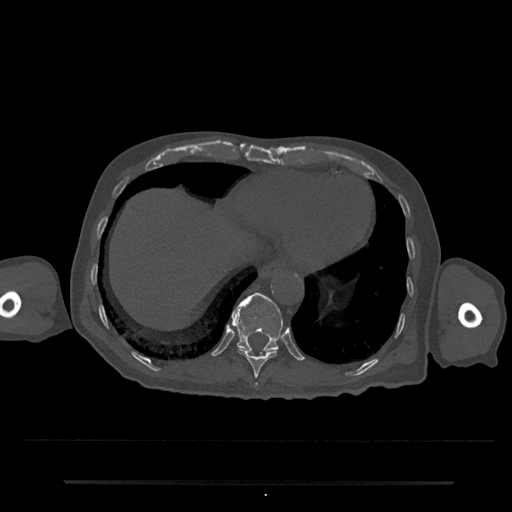
CT including the spine, one axial slice; reconstruction kernel Br40s/3; 120 kVp; bone window (W 1800 / L 400 HU); 0.5 mm slice thickness; 512 × 512 image matrix, field of view 427 × 427 mm. Patient: male, 74 years. Case-level facts recorded for this patient, not image findings: primary cancer: prostate.
Outlined on this slice (semi-automatically segmented with operator editing):
- T10 vertebra: box from (x=237, y=348) to (x=277, y=386) px
- T11 vertebra: (x=231, y=292)–(x=283, y=354)